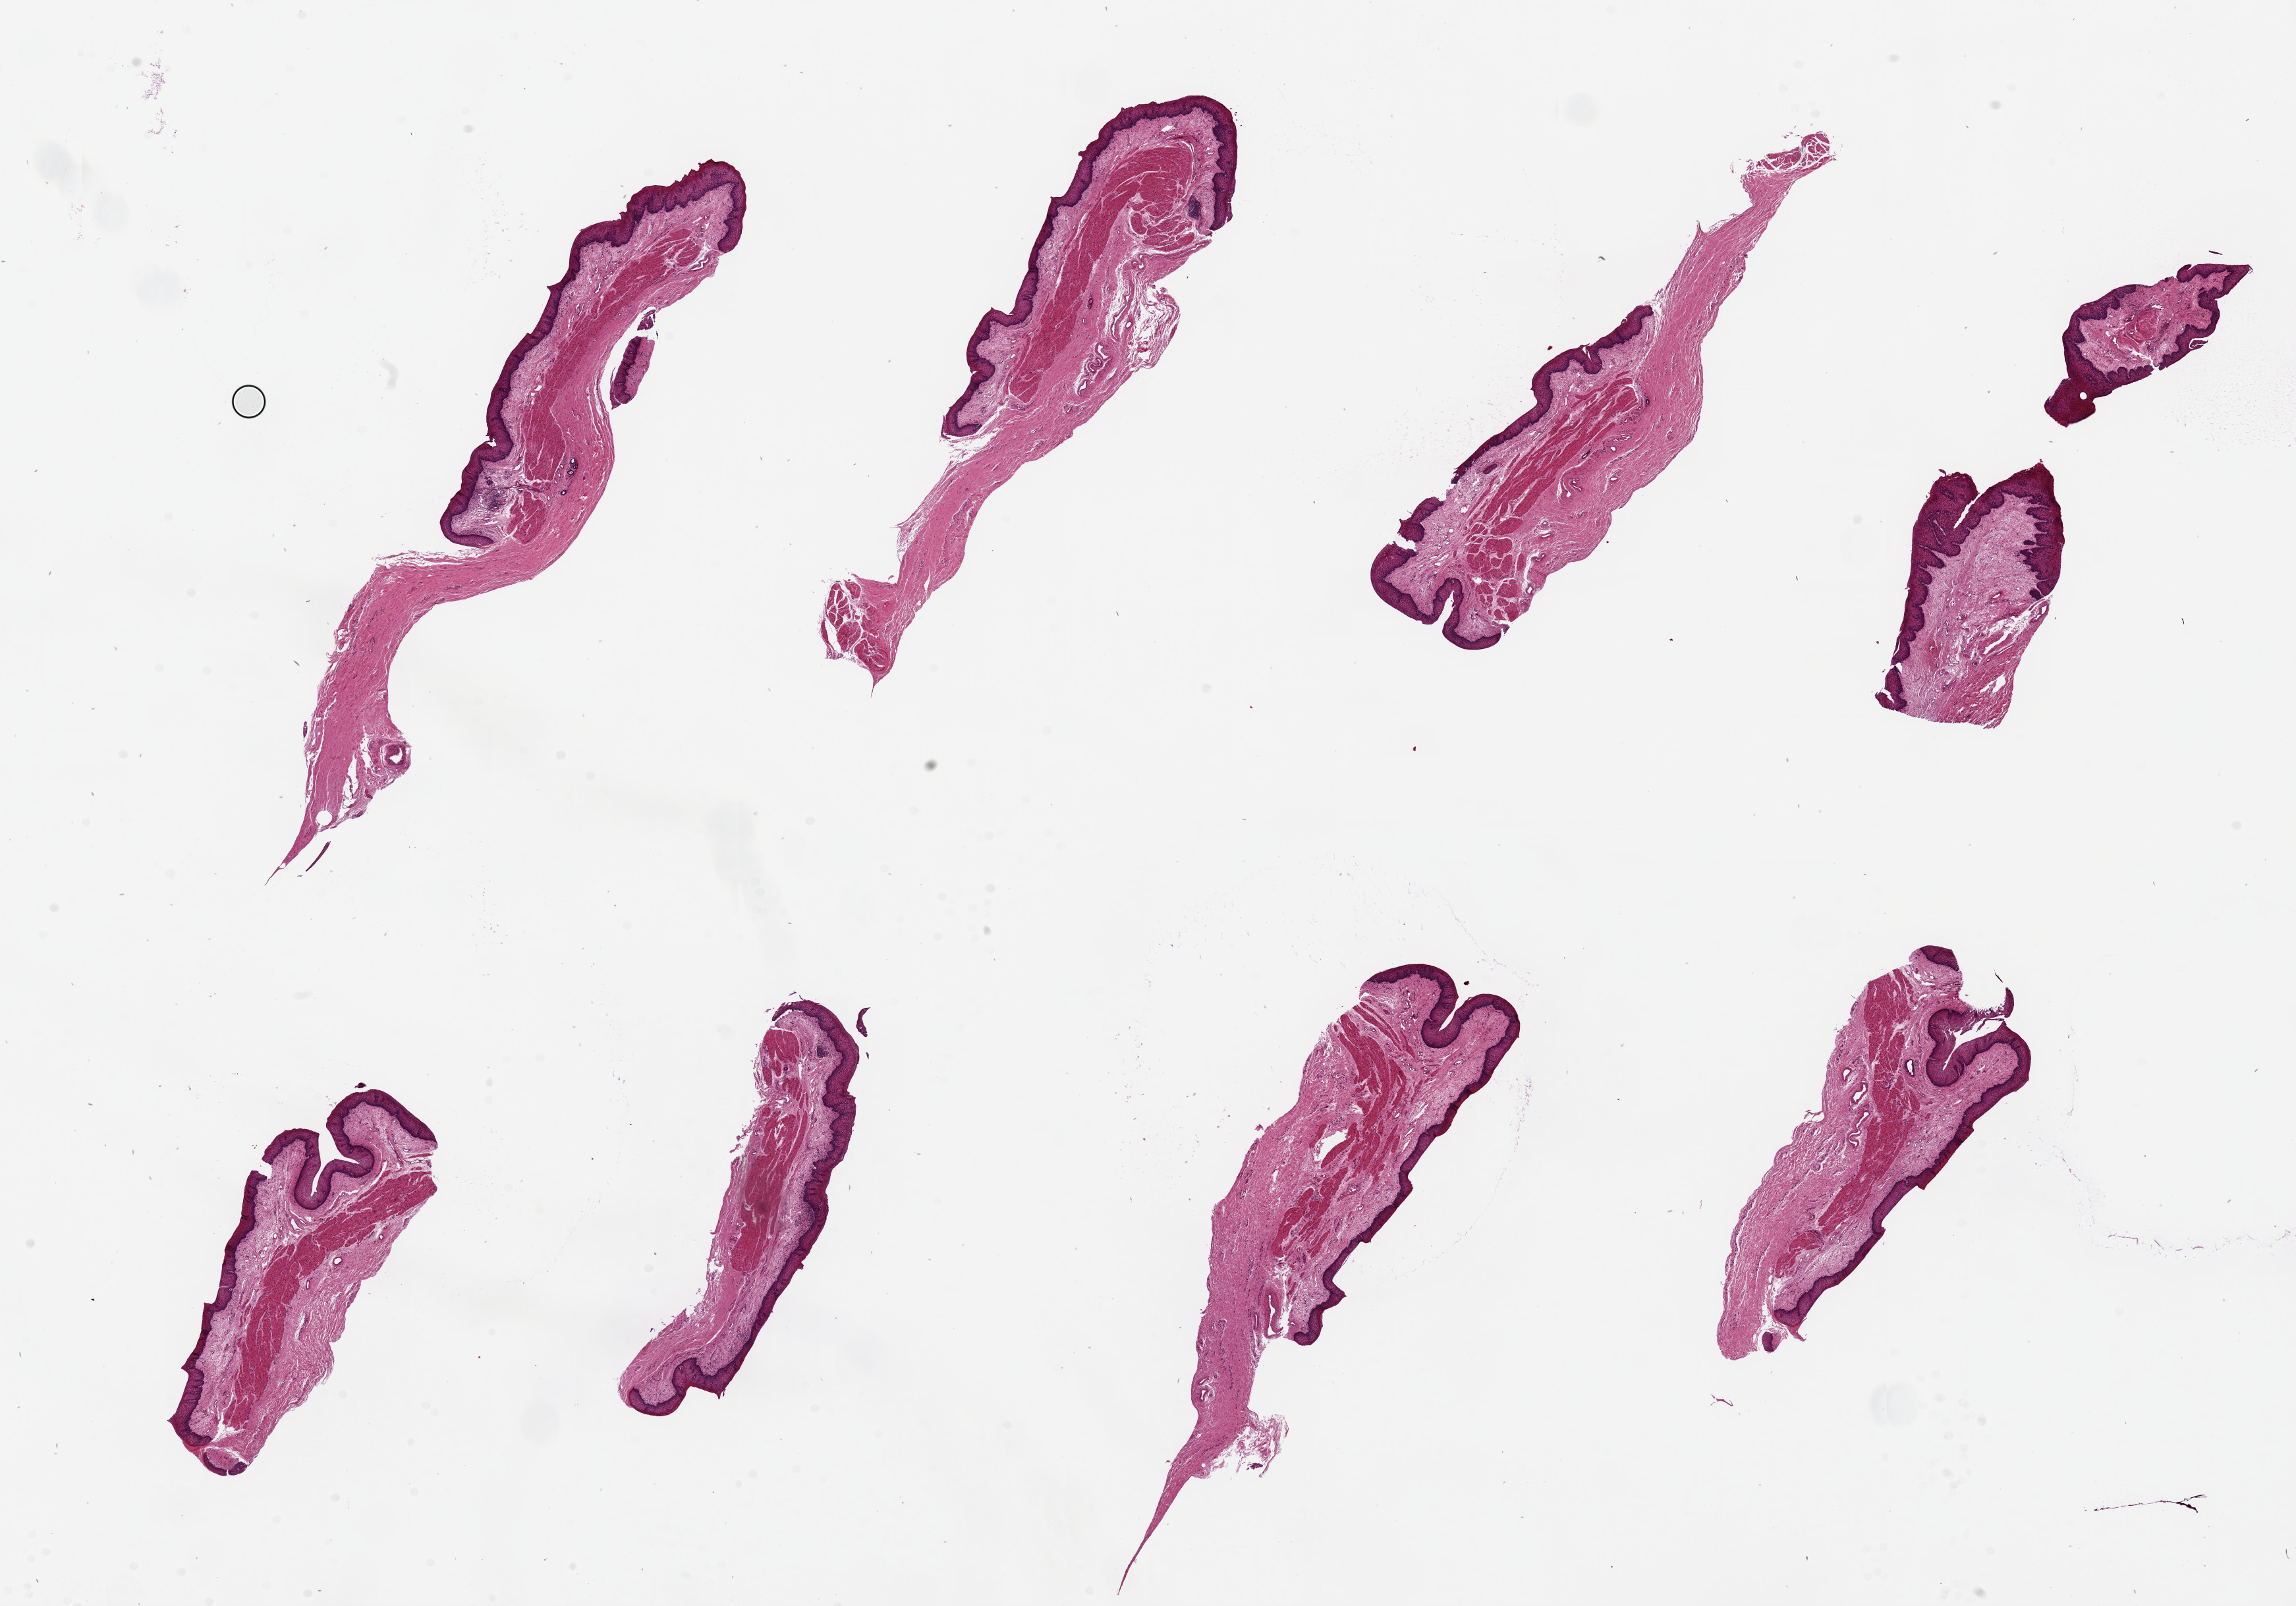
Whole-slide image, H&E stain — a low-resolution overview of the entire scanned area, about 27.6 x 19.3 mm (acquisition: 20x scan); PAXgene-fixed paraffin-embedded (PFPE) section; sampled site (target tissue): esophageal mucous membrane; tissue donor sample. Donor: female.
* reviewer comment on this tissue sample: 8 pieces, up to 10x2mm; good mucosa